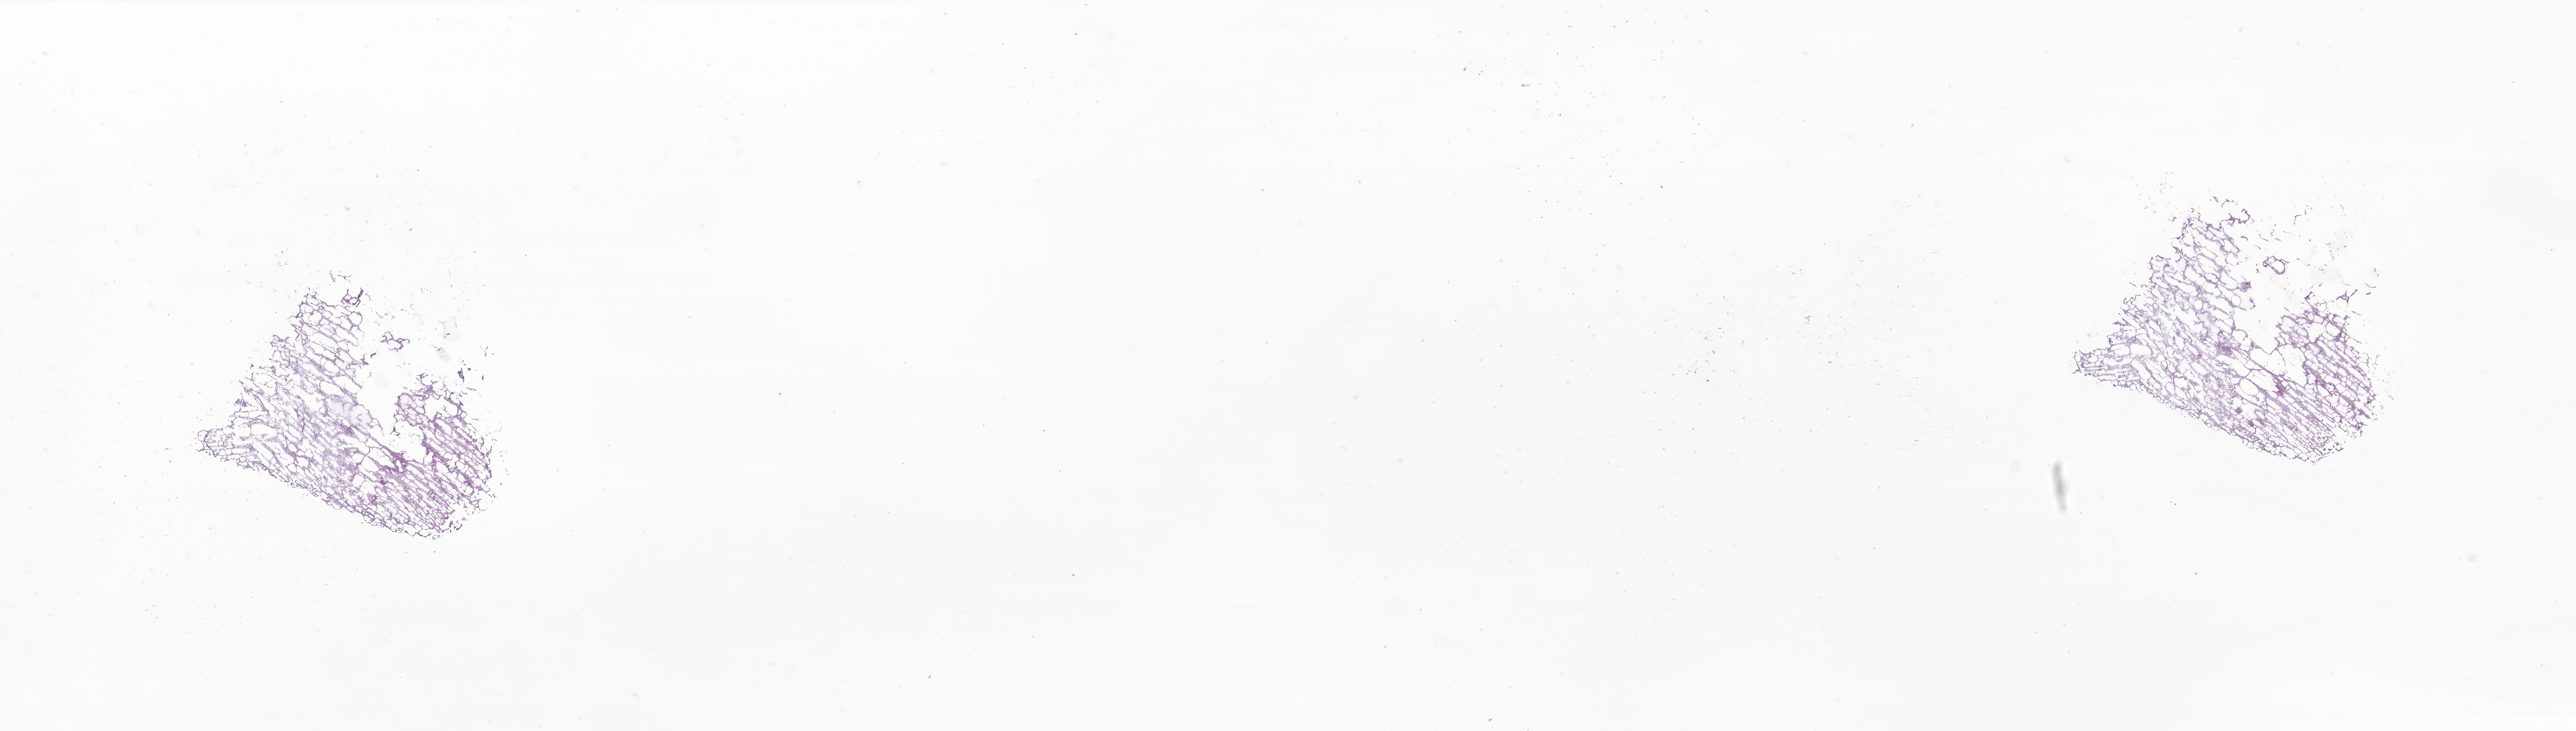
Whole-slide image, hematoxylin and eosin (H&E) stain of tumor tissue from the brain — shown as a low-resolution overview of the whole scanned area (about 25.4 x 7.2 mm). Cryosection (OCT / tissue freezing medium). Patient: male, age 209 months (17 years 5 months).
- recorded diagnosis: Pilocytic astrocytoma